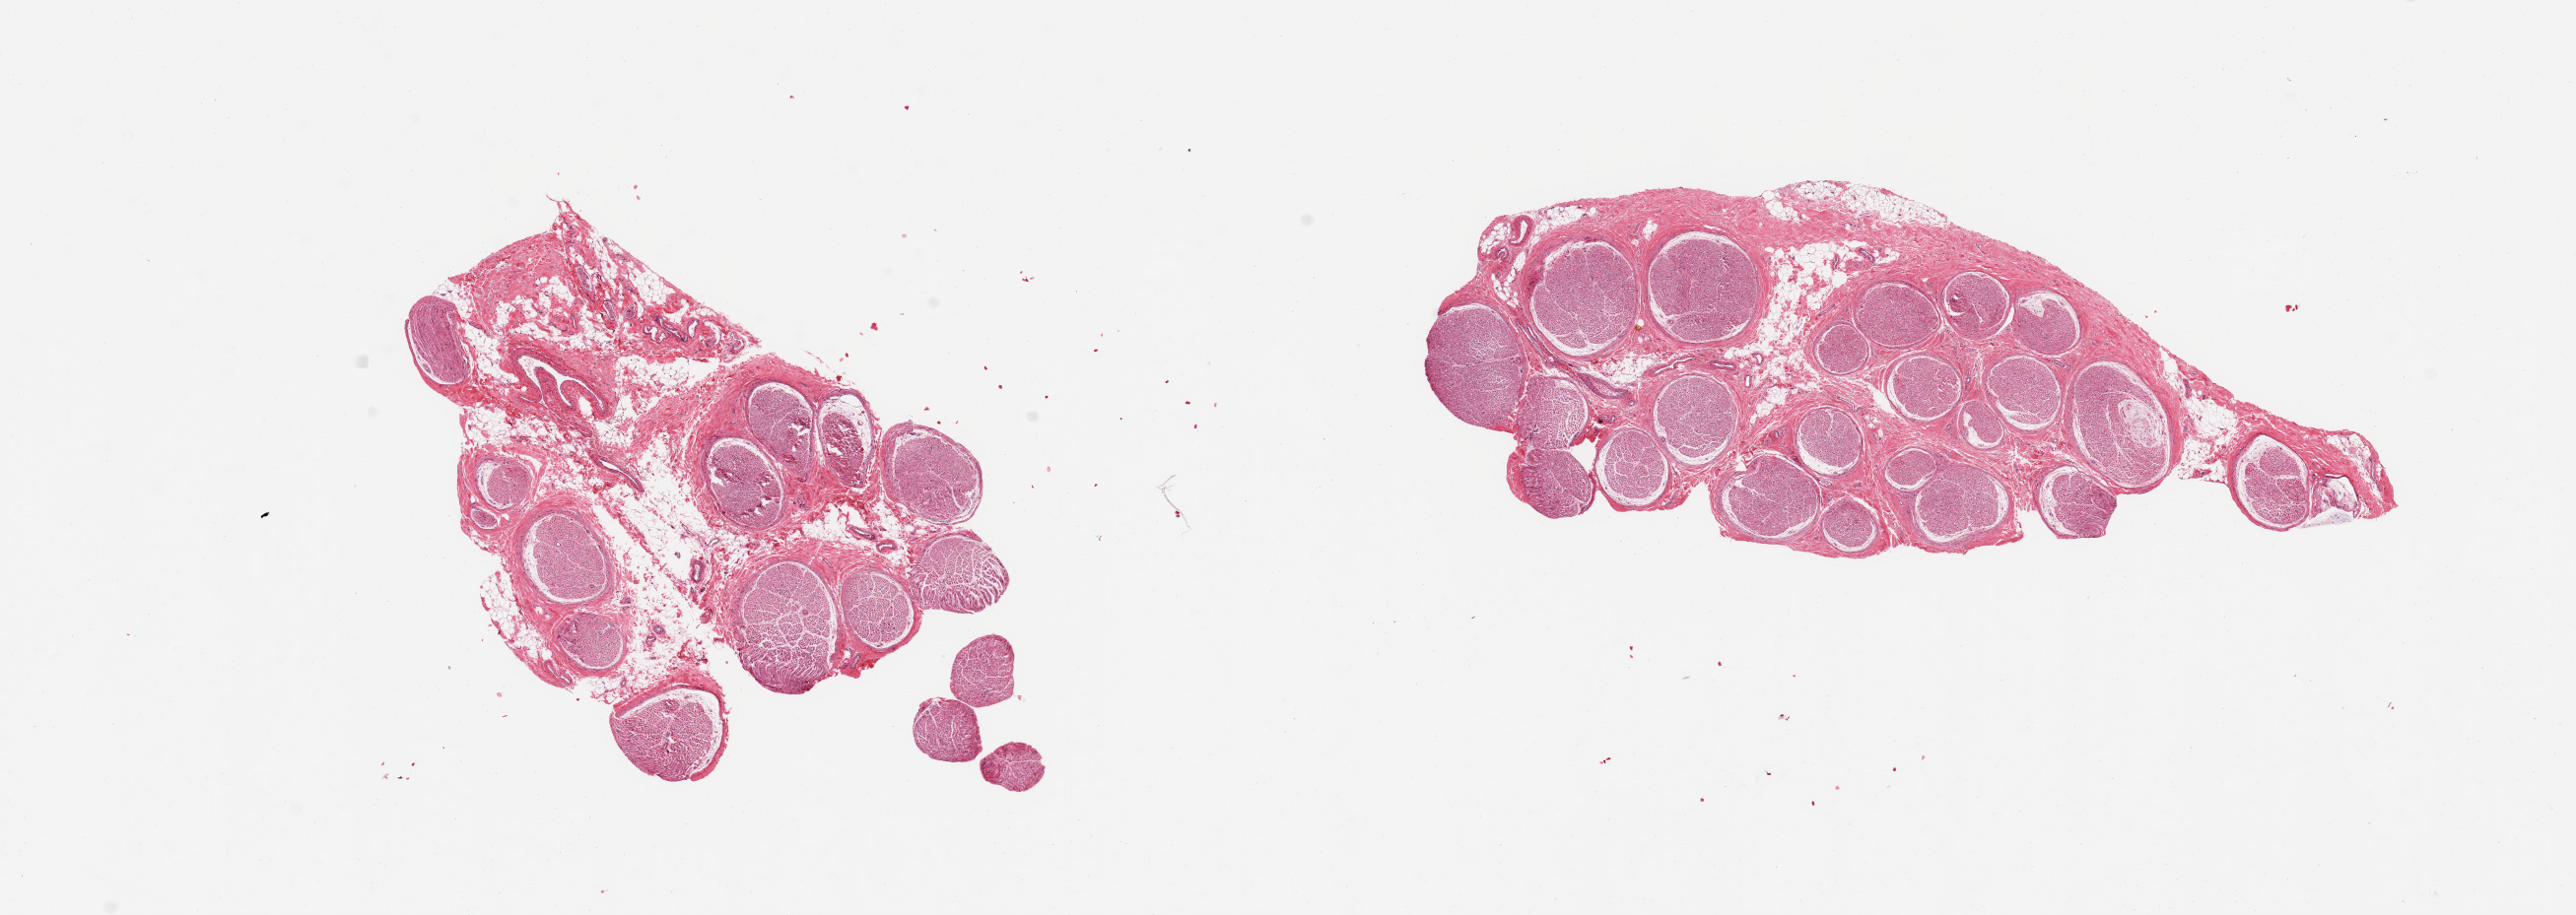
Digitized haematoxylin and eosin-stained section, brightfield, whole scanned area (about 20.7 x 7.3 mm, slide scanned at 20x) shown as a low-resolution overview. PAXgene-fixed paraffin-embedded (PFPE) section. Target tissue: tibial nerve. Donor tissue sample.
* pathologist's review note for this sample: 2 pieces; 1 piece is ~50% fat/fibrovascular tissue, 2nd is 10% fat